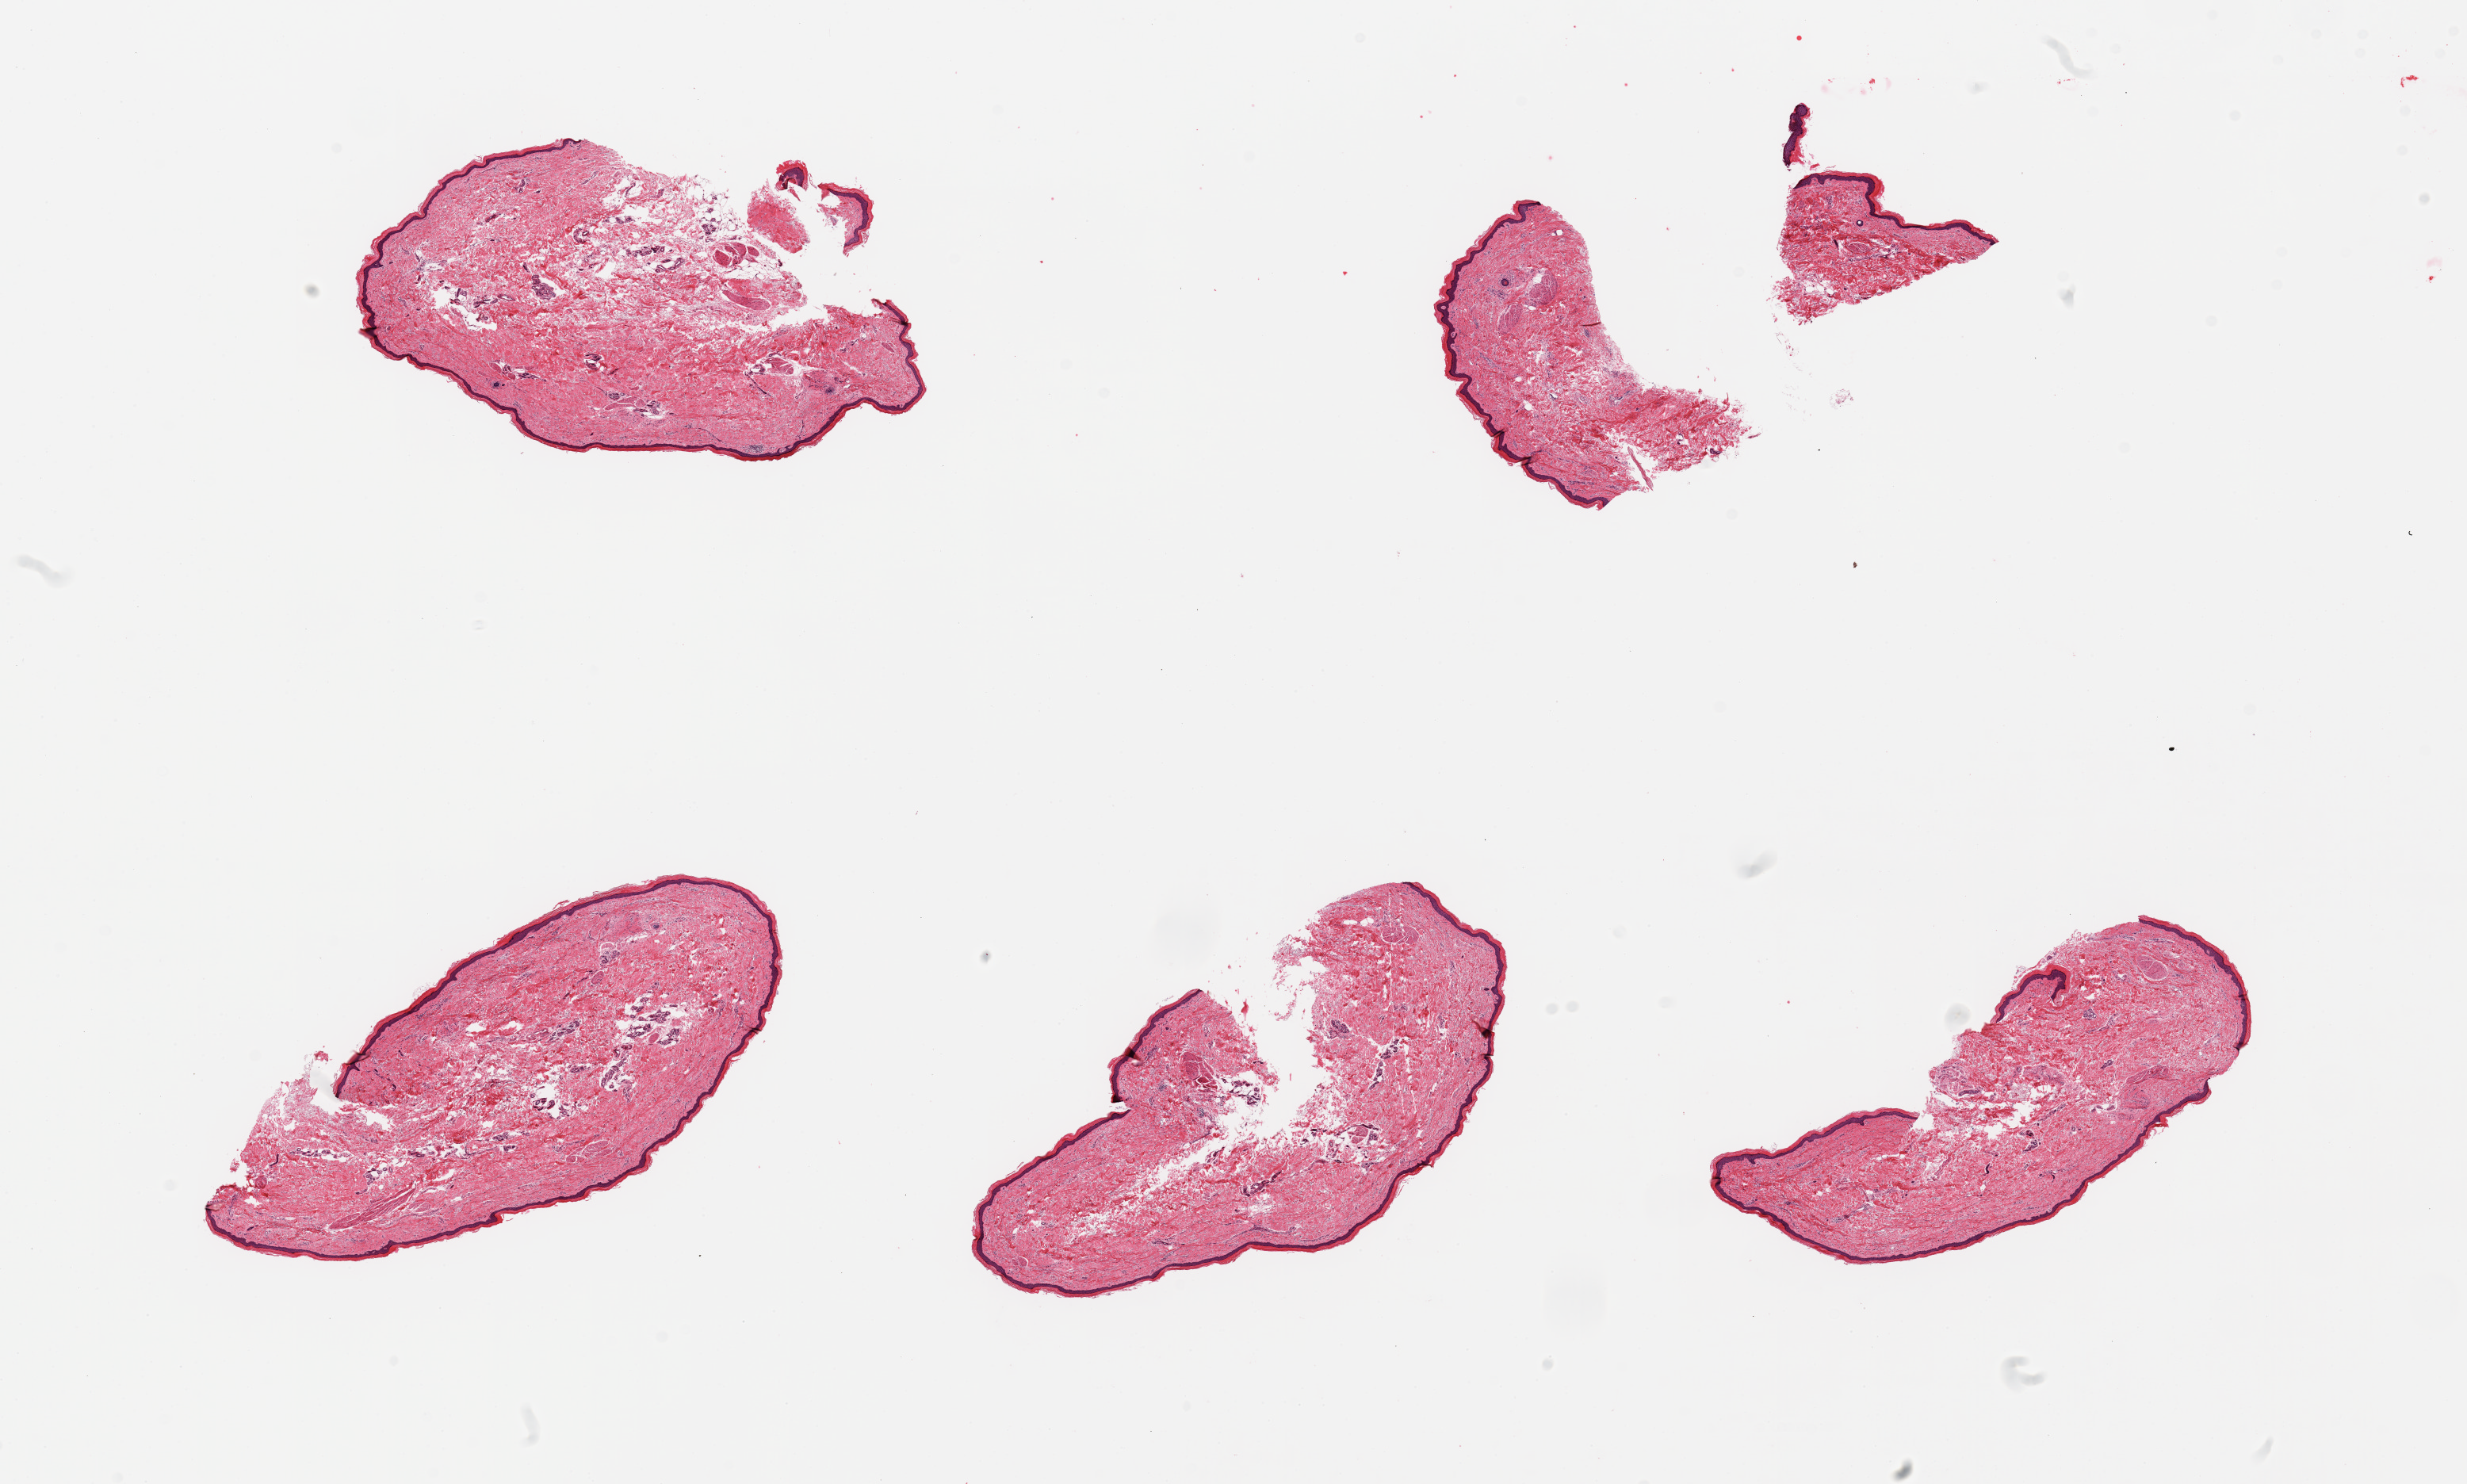
Digitized haematoxylin and eosin-stained section — whole scanned area (about 24.6 x 14.8 mm) shown as a low-resolution overview; PAXgene-fixed, paraffin-embedded tissue; section of skin of lower leg (target tissue); donor tissue sample. Female donor.
Review note (as recorded): 6 pieces; well trimmed, epidermis measures 32 microns, focal parakeratosis.